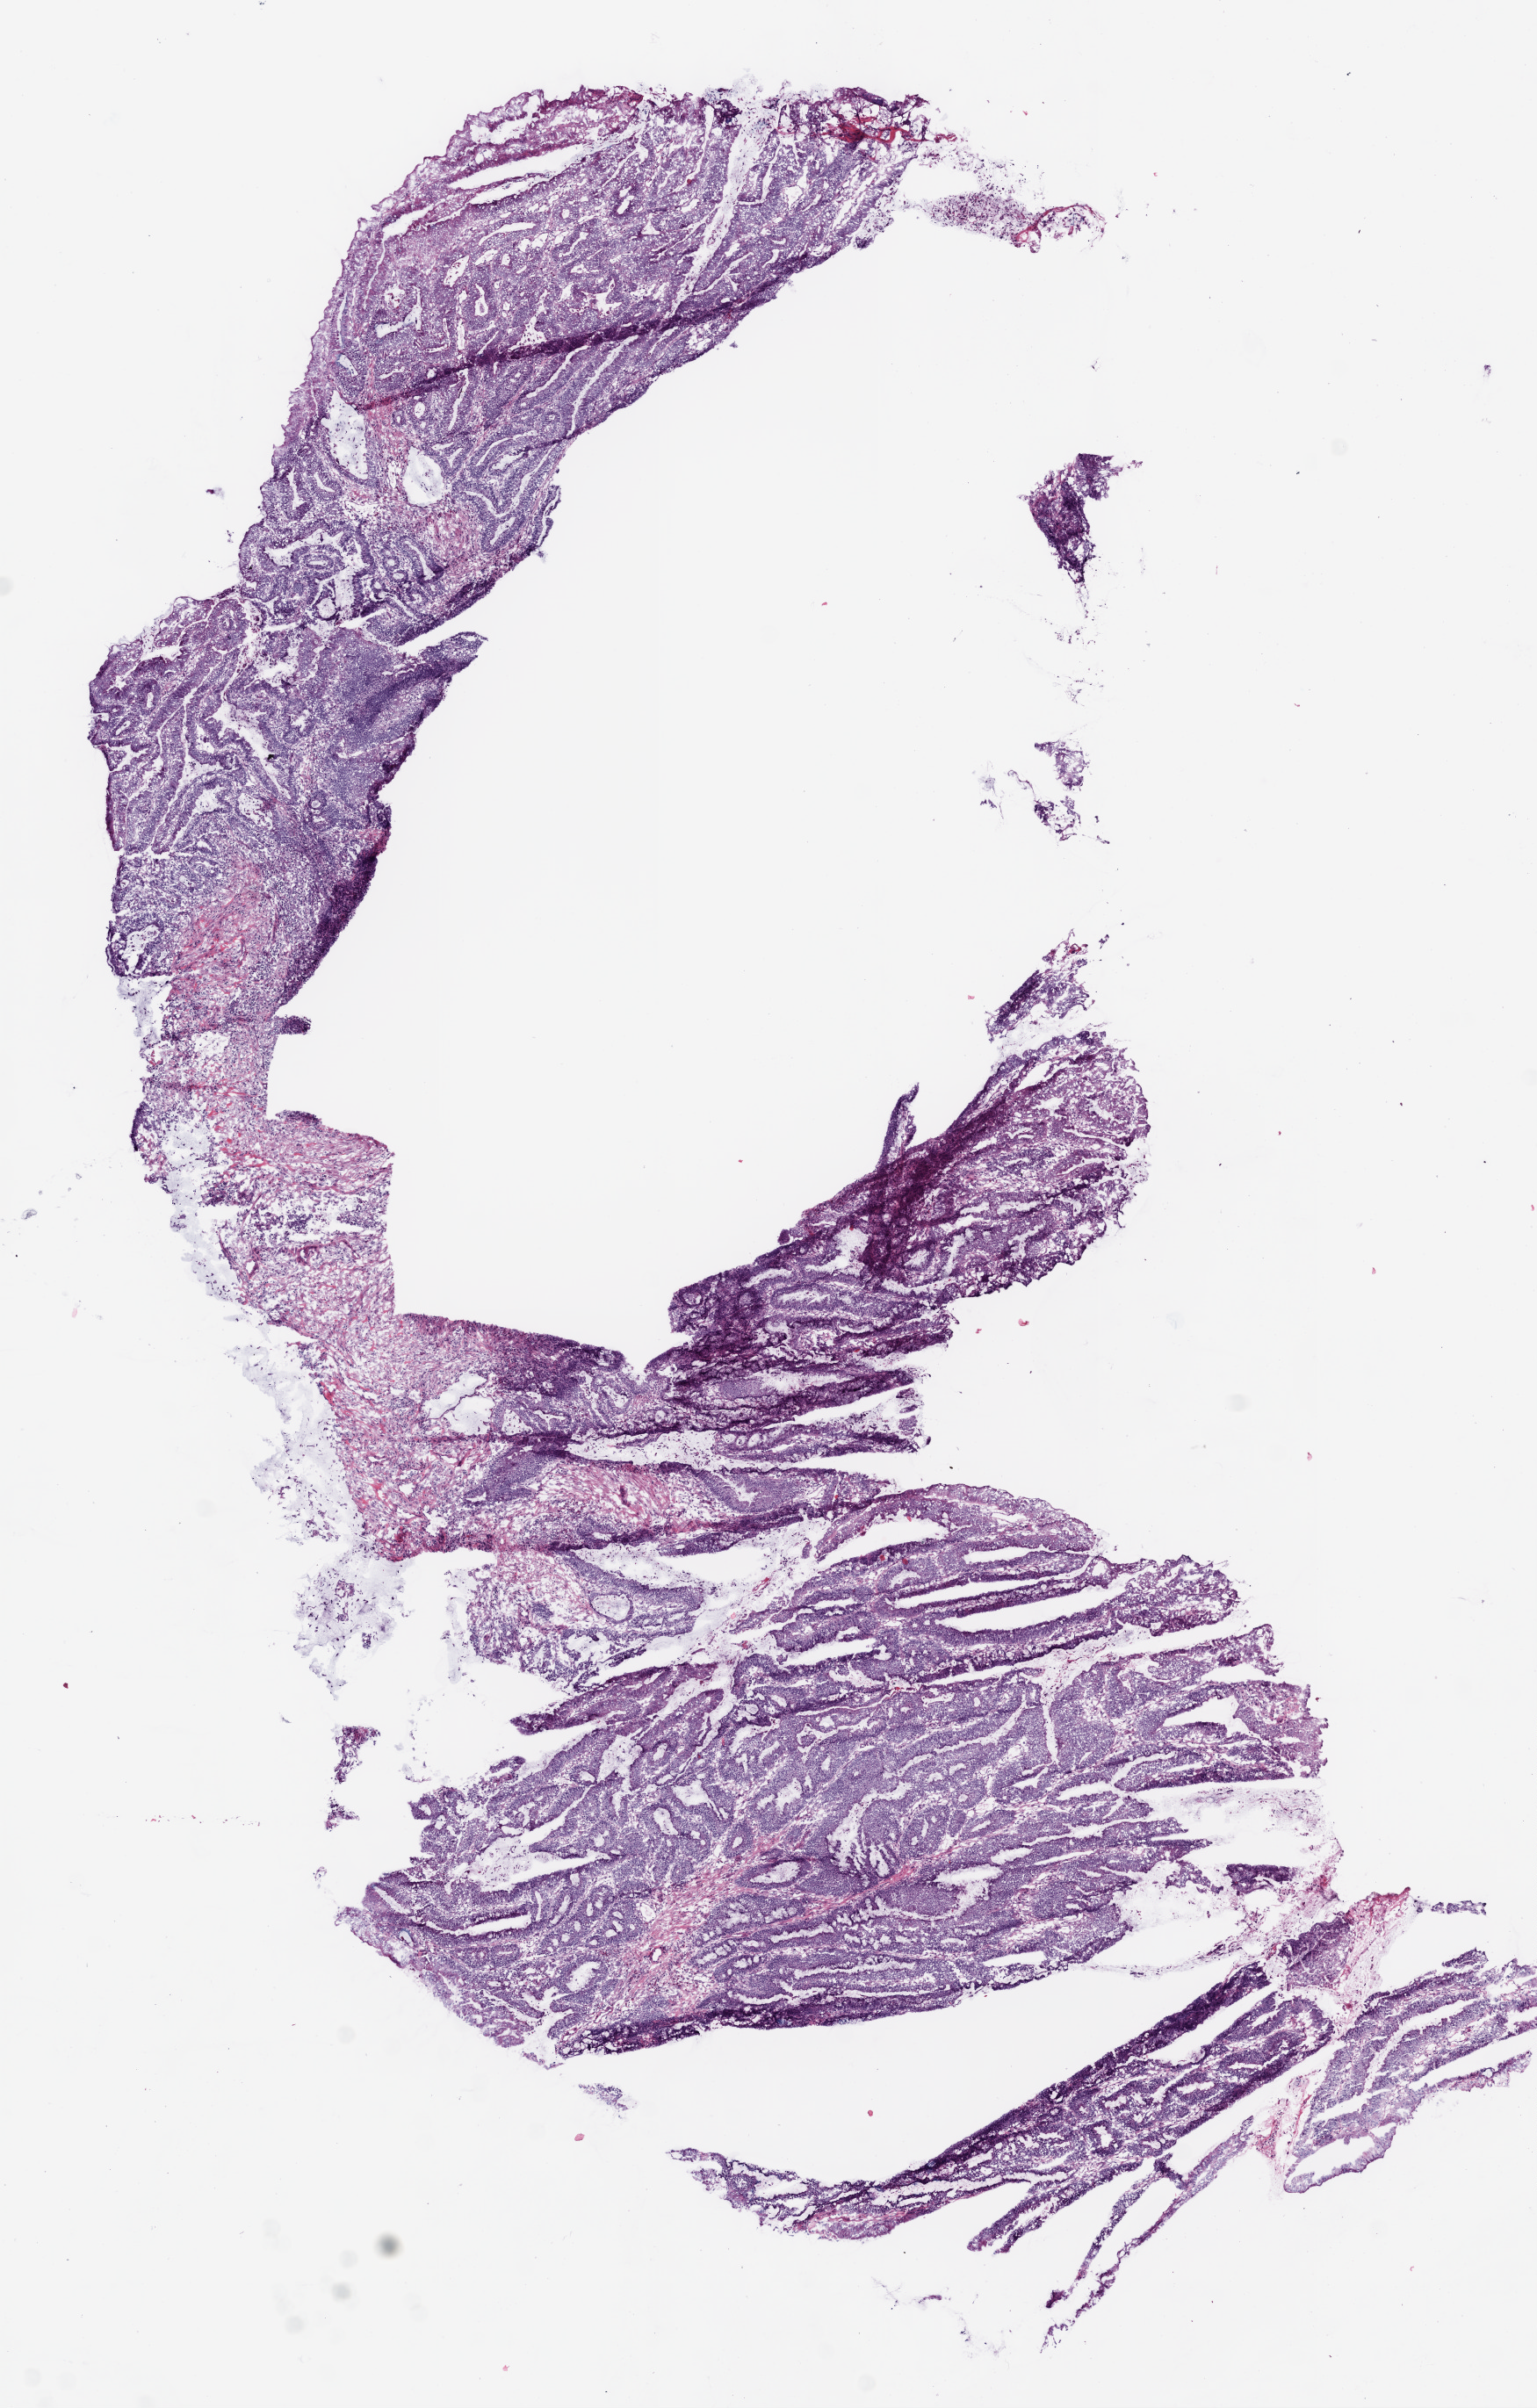
H&E whole-slide image, low-resolution overview of the scanned area, about 7.0 x 11.0 mm. Frozen section from the bottom of the tissue portion. Colon, primary tumour sample. Male, age 42 years at initial diagnosis.
Pathologic diagnosis: Adenocarcinoma, NOS (cecum).